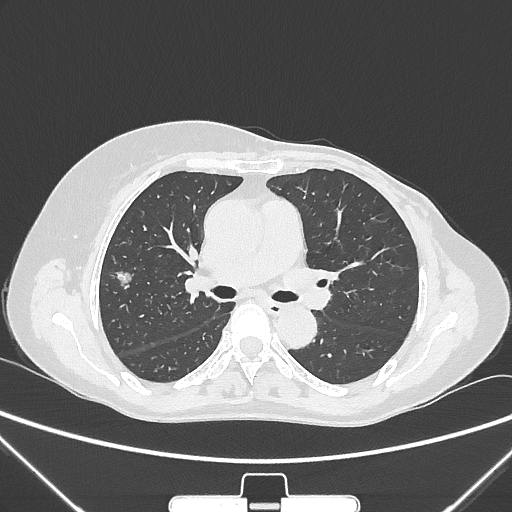
Chest CT, one axial slice; position 153 of 265 along the scan axis; lung window (W 1500 / L -600 HU); 1 mm slice thickness; 512 × 512 image matrix, field of view 350 × 350 mm. Female patient, age 64 years. From the clinical record (not read from this slice): clinical TNM (as recorded): T1c N0 M0; histopathological grade: G1-2.
Outlined on this slice (rectangle marked by the reading radiologist):
- lung tumour (recorded histology: adenocarcinoma): bounding box (x1, y1, x2, y2) in pixels: (110, 259, 131, 292)